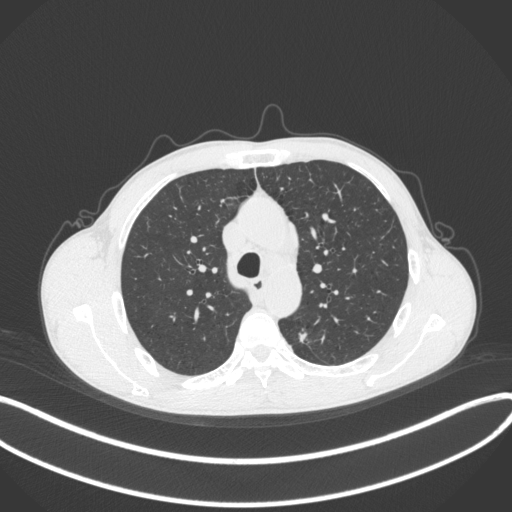
Chest CT, one axial slice. Reconstruction kernel B31f. 120 kVp. Lung window (W 1500 / L -600 HU). 512 × 512 image matrix, field of view 400 × 400 mm. Male patient, age 51 years. From the clinical record (not read from this slice): clinical TNM (as recorded): T2a N1 M1.
Annotated regions visible in this slice (rectangle marked by the reading radiologist):
- lung tumour (recorded histology: adenocarcinoma): bounding box [x1, y1, x2, y2] px = [293, 326, 314, 347]